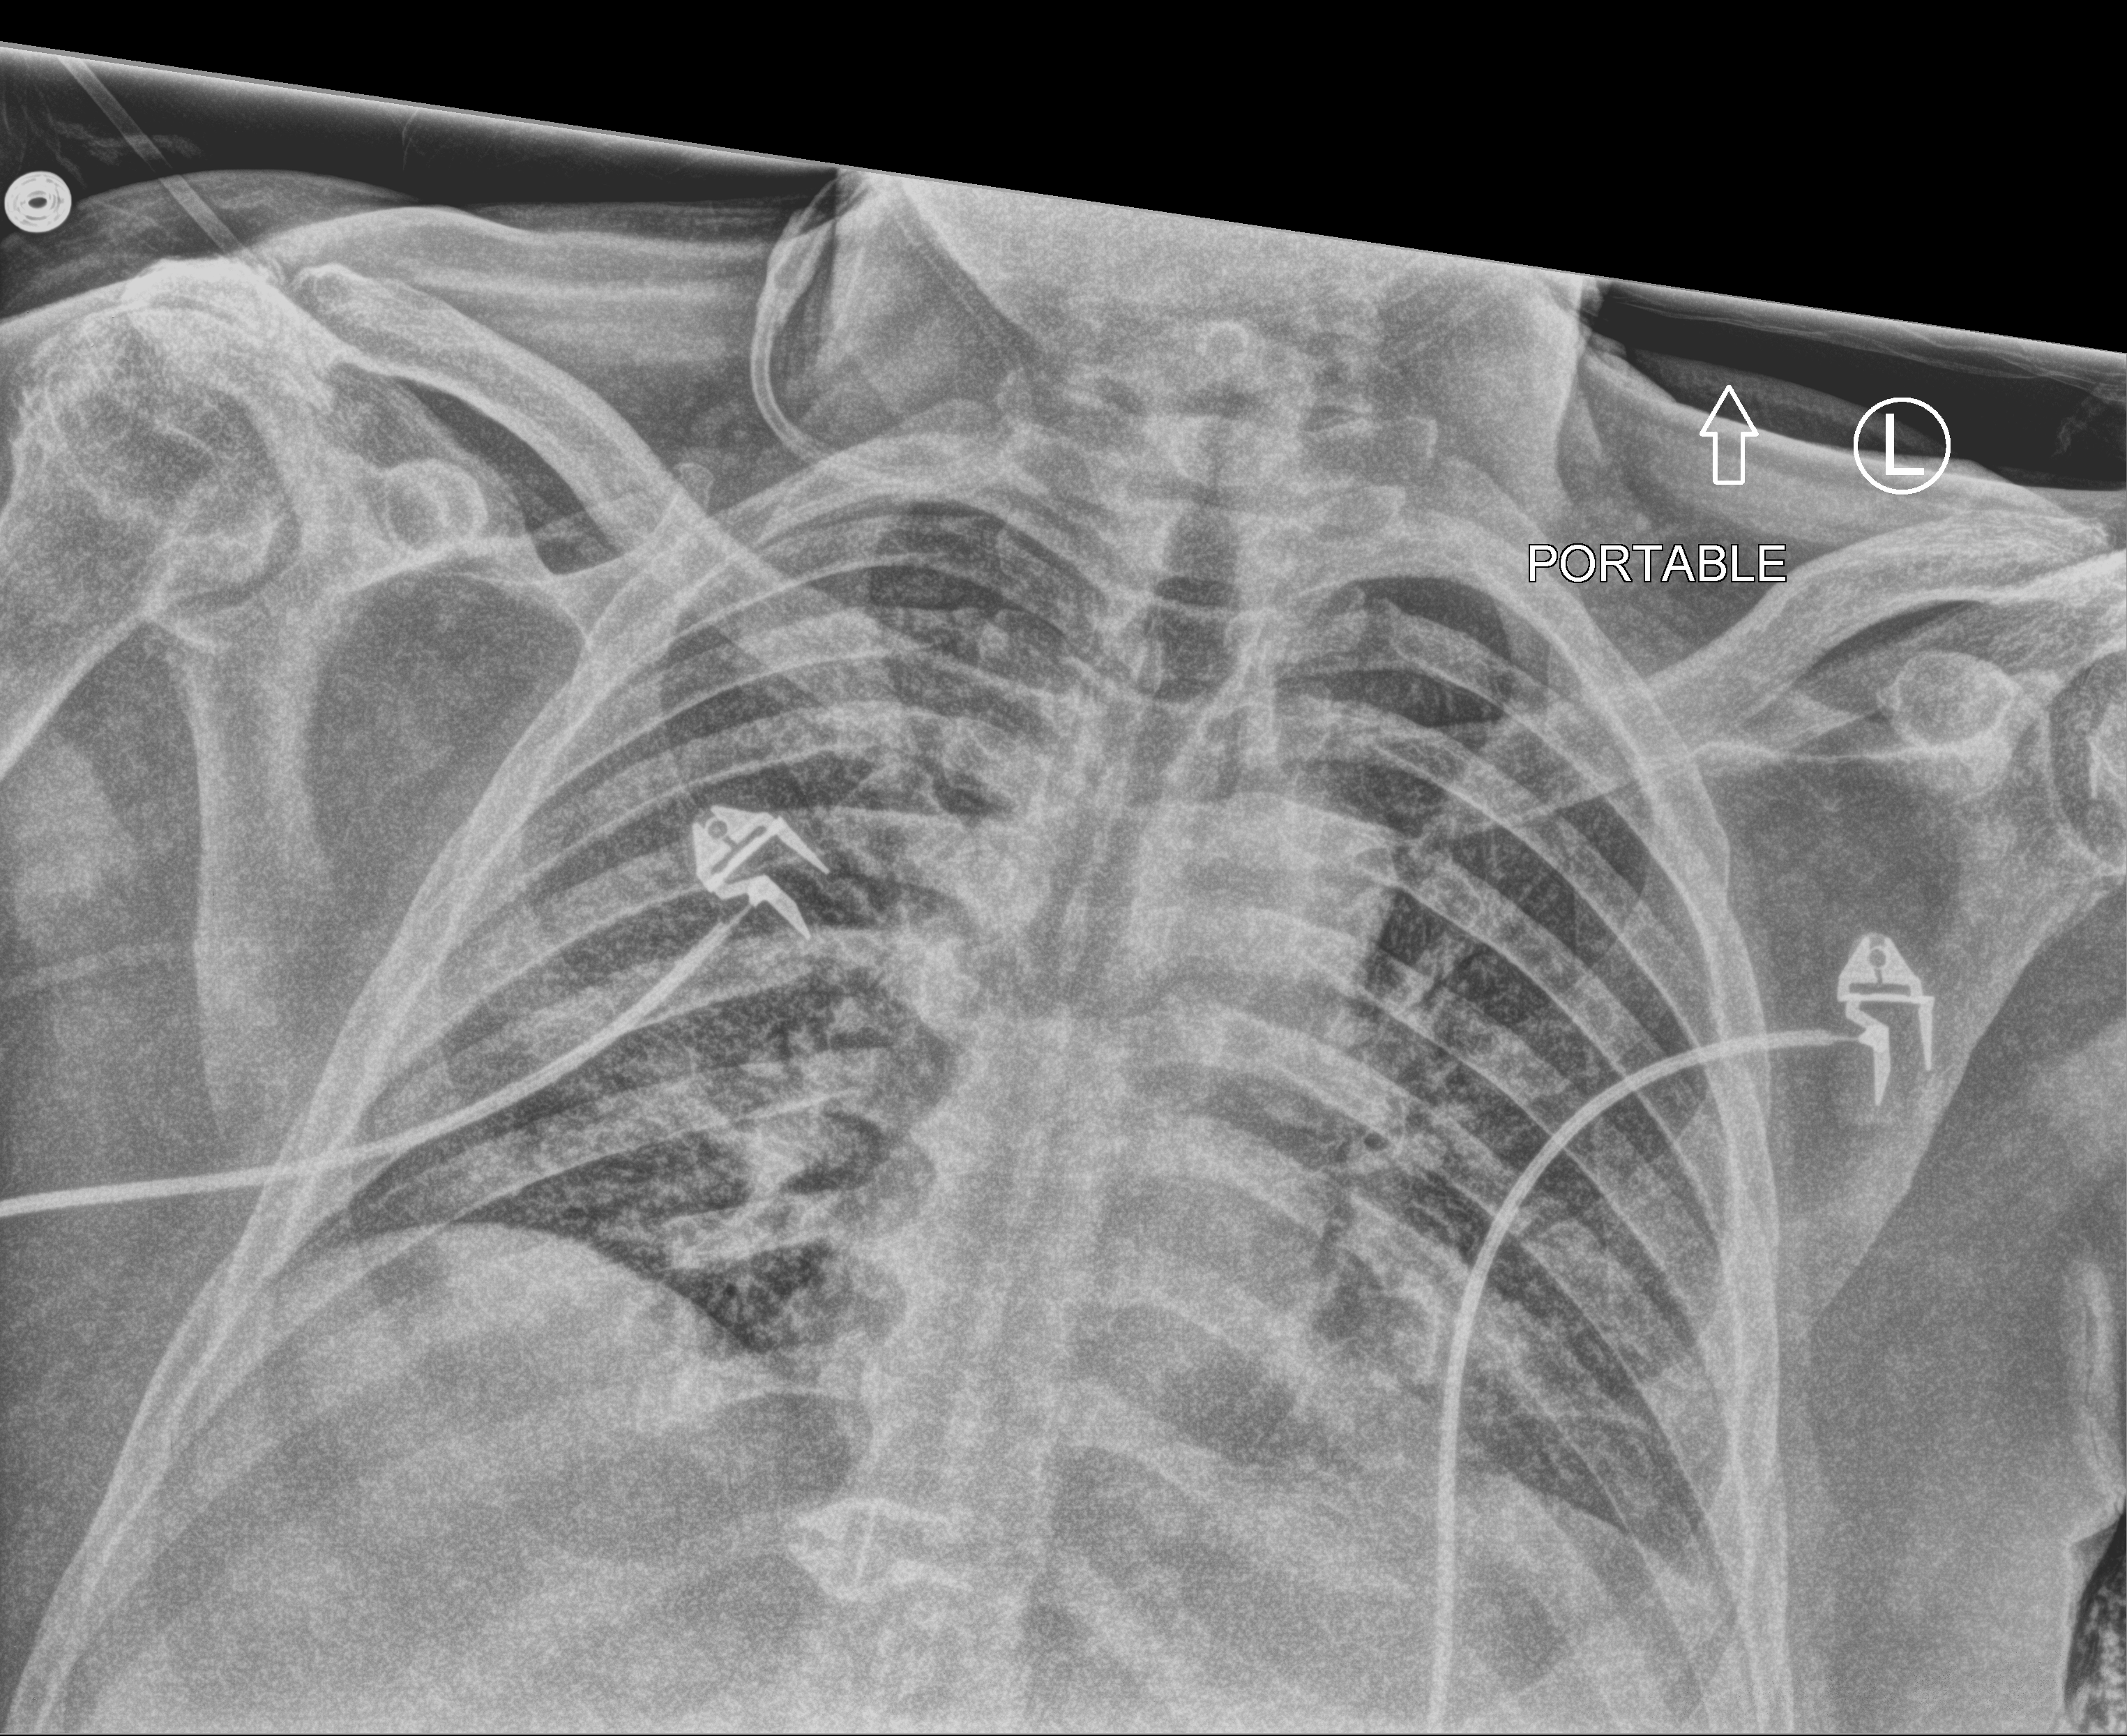
Chest X-ray (portable), anteroposterior (AP) projection. Patient hospitalised with COVID-19; male, aged 75–90 years.
Admission-level facts for this patient (not findings on this image; timing relative to this image not recorded): mechanically ventilated during this hospital stay: yes; admitted to intensive care during this hospital stay: yes; chronic kidney disease (admission record): no.